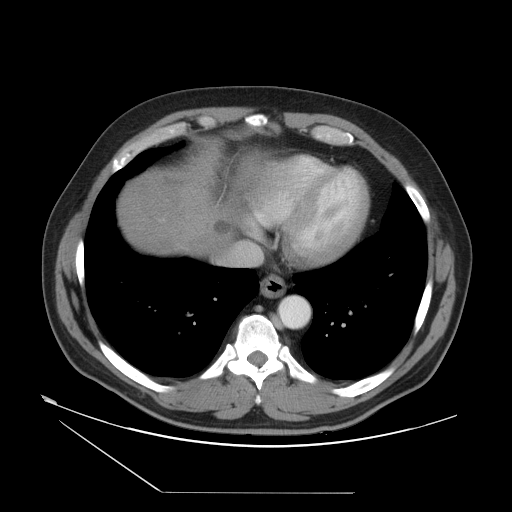
Contrast-enhanced abdominal CT, one axial slice; slice 48 of 55 in the series (ordered by position); reconstruction kernel STANDARD; 120 kVp; intravenous contrast given; soft-tissue window (W 400 / L 40 HU); 5 mm slice thickness; 512 × 512 image matrix, field of view 454 × 454 mm. Male patient, age 59 years. From the clinical record (not read from this slice): diagnosis: colorectal cancer liver metastases, imaged before liver resection; multiple liver metastases: yes.
Outlined on this slice (expert manual segmentation):
- hepatic veins: bounding box (x1, y1, x2, y2) in pixels: (232, 200, 265, 265)
- liver: (121, 163, 231, 252)
- planned liver remnant (the part of the liver to remain after resection): (120, 178, 193, 251)
- liver metastasis: (217, 219, 229, 239)